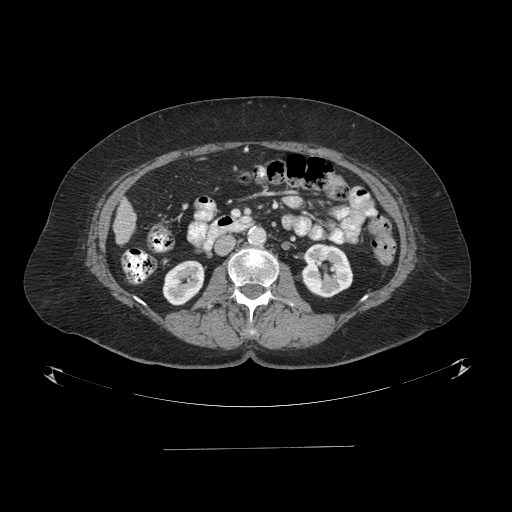
Contrast-enhanced abdominal CT (liver protocol), one axial slice; position 19 of 103 along the scan axis; reconstruction kernel STANDARD; 120 kVp; one of 2 acquisitions stored at this slice position; soft-tissue window (W 400 / L 40 HU); 2.5 mm slice thickness; 512 × 512 image matrix, field of view 500 × 500 mm. From the clinical record (not read from this slice): diagnosis: hepatocellular carcinoma (patient treated with transarterial chemoembolisation; whether this scan precedes or follows treatment is not stated here); TNM stage (as recorded): Stage-IIIA; Child-Pugh class: A.
Annotated regions visible in this slice (semi-automatically segmented with operator editing):
- liver parenchyma outside the tumour (the mass and vessels are separate outlines, so this box may not span the whole liver): bounding box (x1, y1, x2, y2) in pixels: (114, 198, 136, 244)